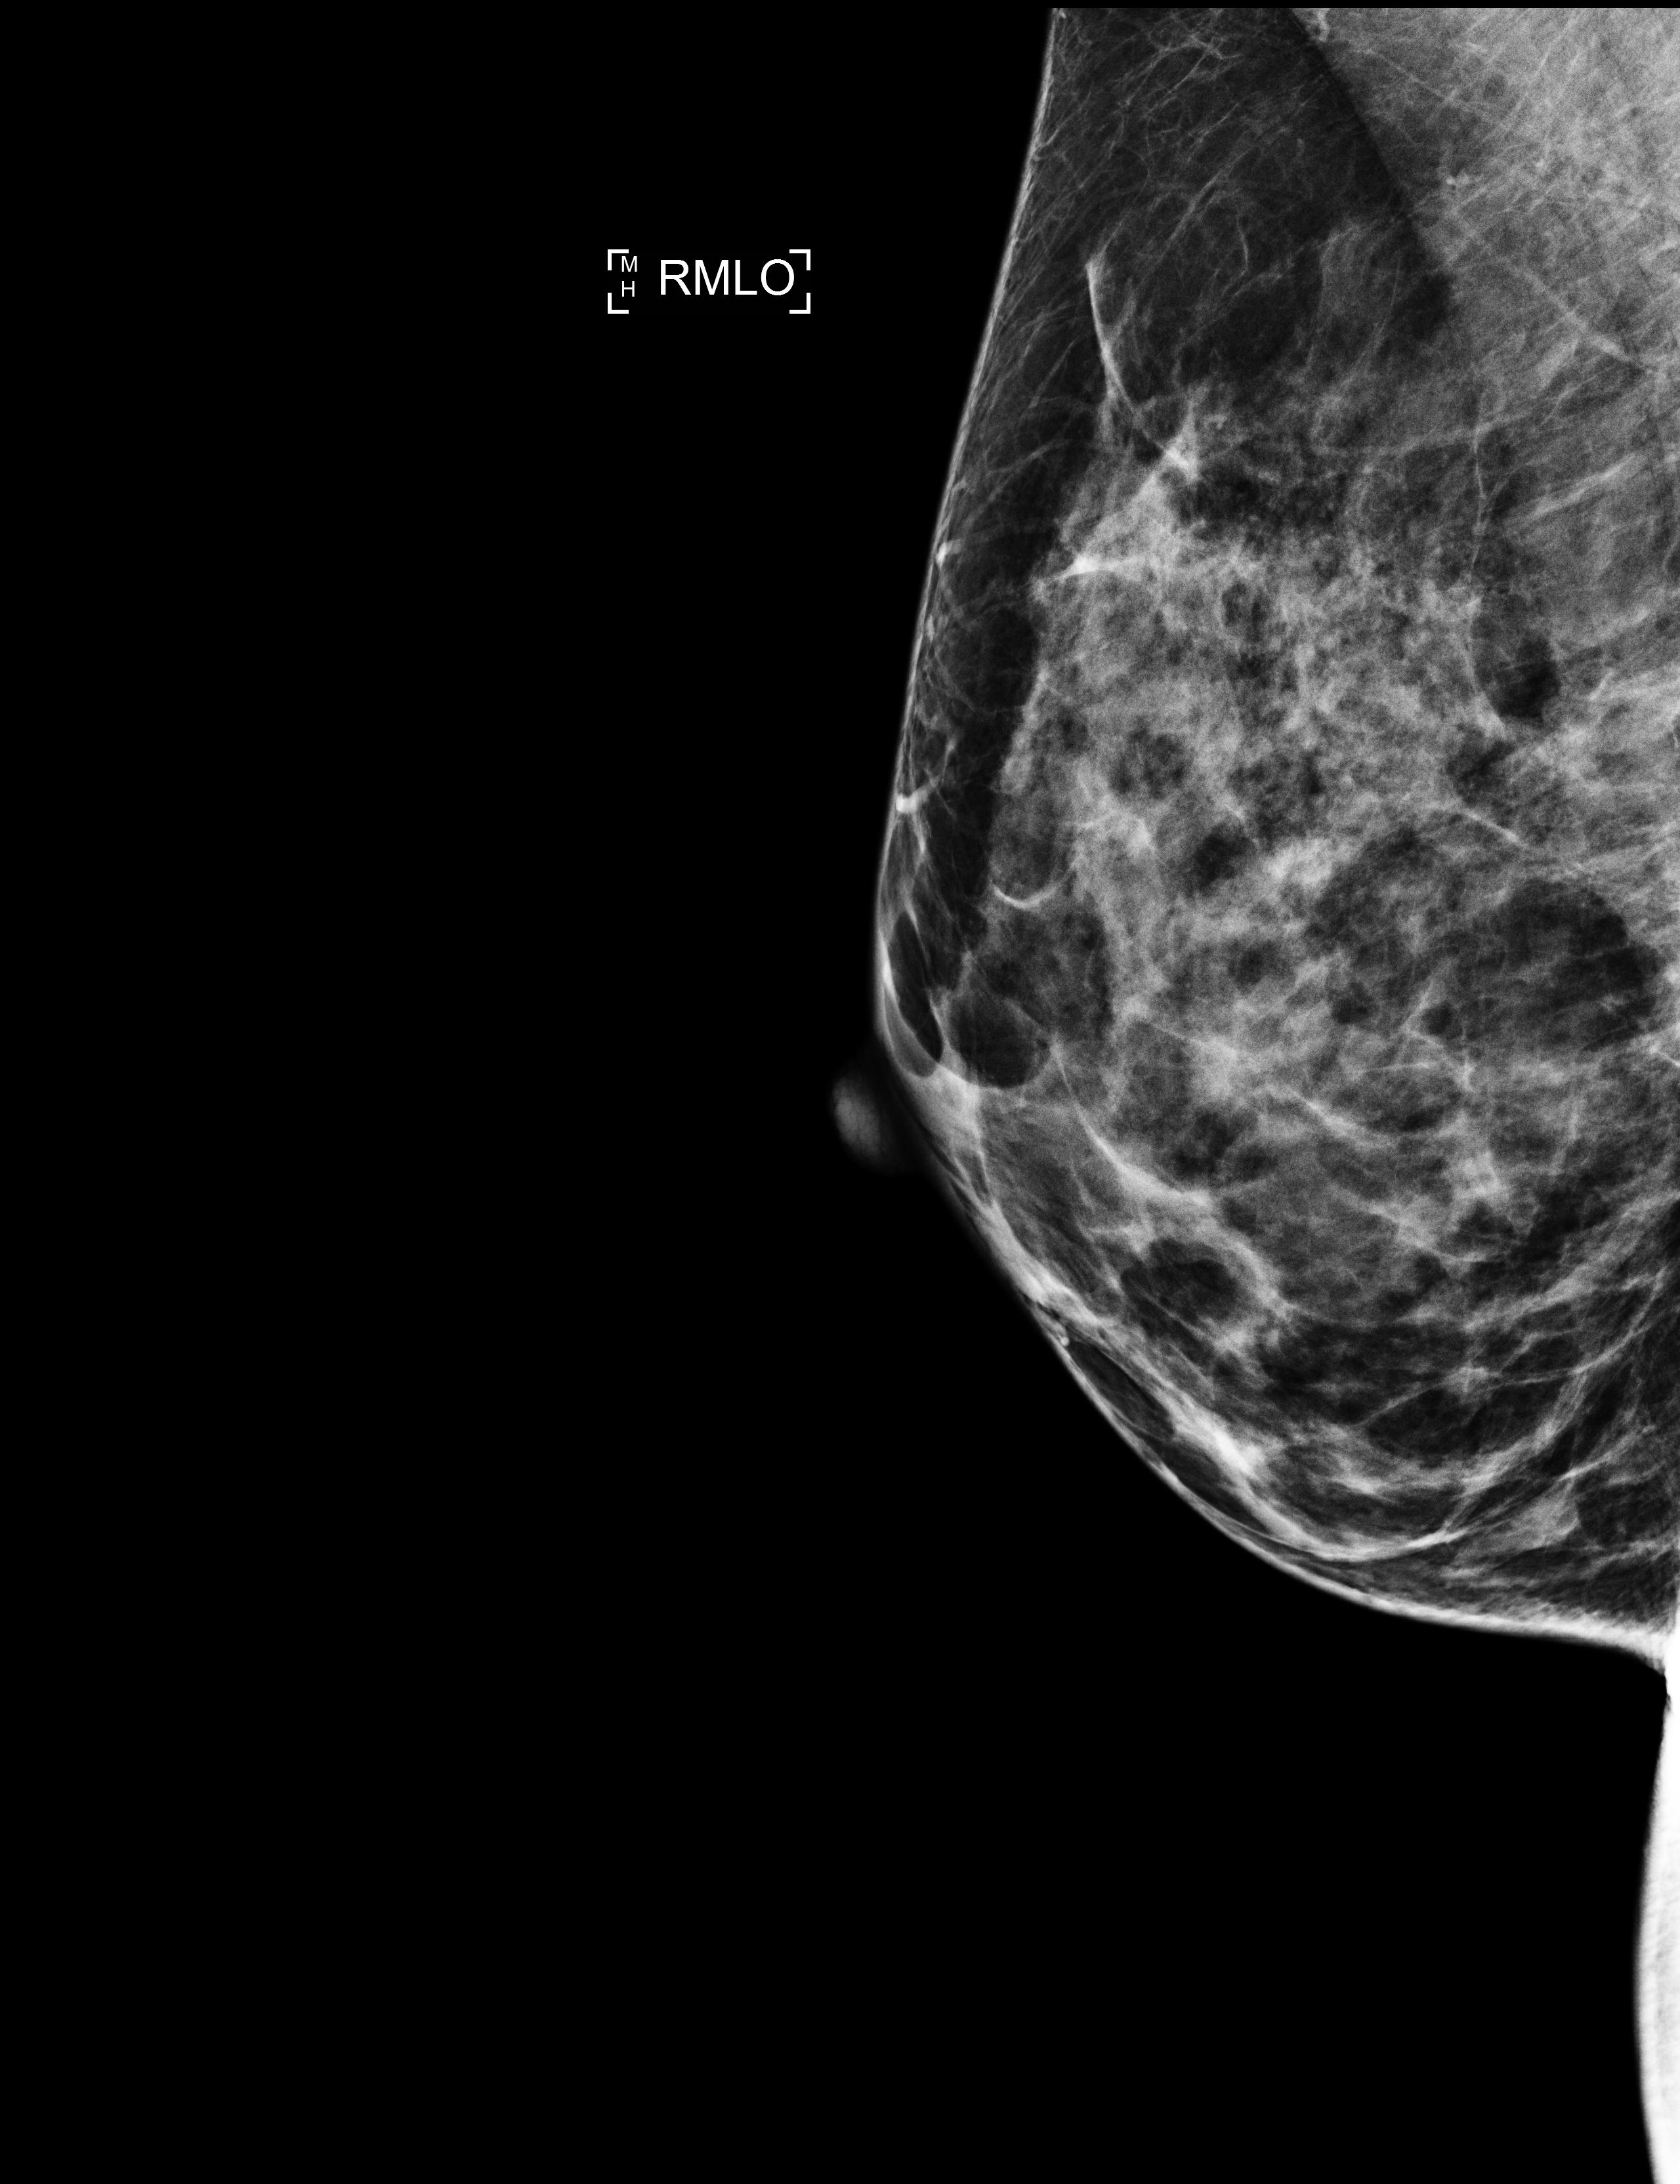
Full-field digital mammogram (FFDM); right breast; mediolateral oblique (MLO) view; screening examination; compressed breast thickness 48 mm; system: Selenia Dimensions. Female patient, age 41 years.
BI-RADS breast density category at the screening exam (both breasts, scale 1–4): 4. Final BI-RADS assessment for this screening round (tomosynthesis exam, both breasts): category 1. Recall: no recall after this screen.